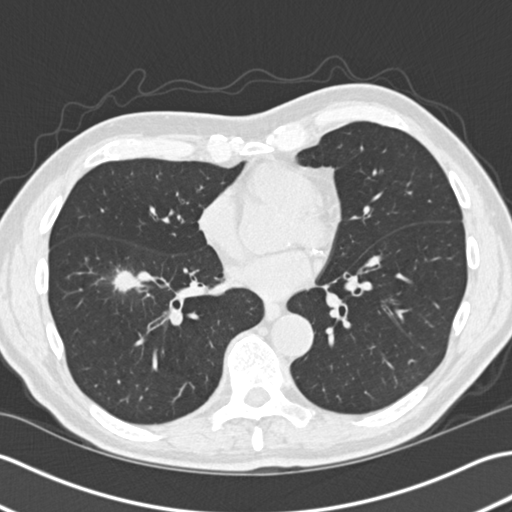
Low-dose screening chest CT, one axial slice; position 71 of 172 along the scan axis; reconstruction kernel B30f; 120 kVp; lung window (W 1500 / L -600 HU); 2 mm slice thickness; 512 × 512 image matrix, field of view 350 × 350 mm.
Outlined on this slice (manually delineated by an expert):
- lesion 1 (tumor, lower lobe of right lung): bounding box [x1, y1, x2, y2] px = [112, 270, 145, 293]